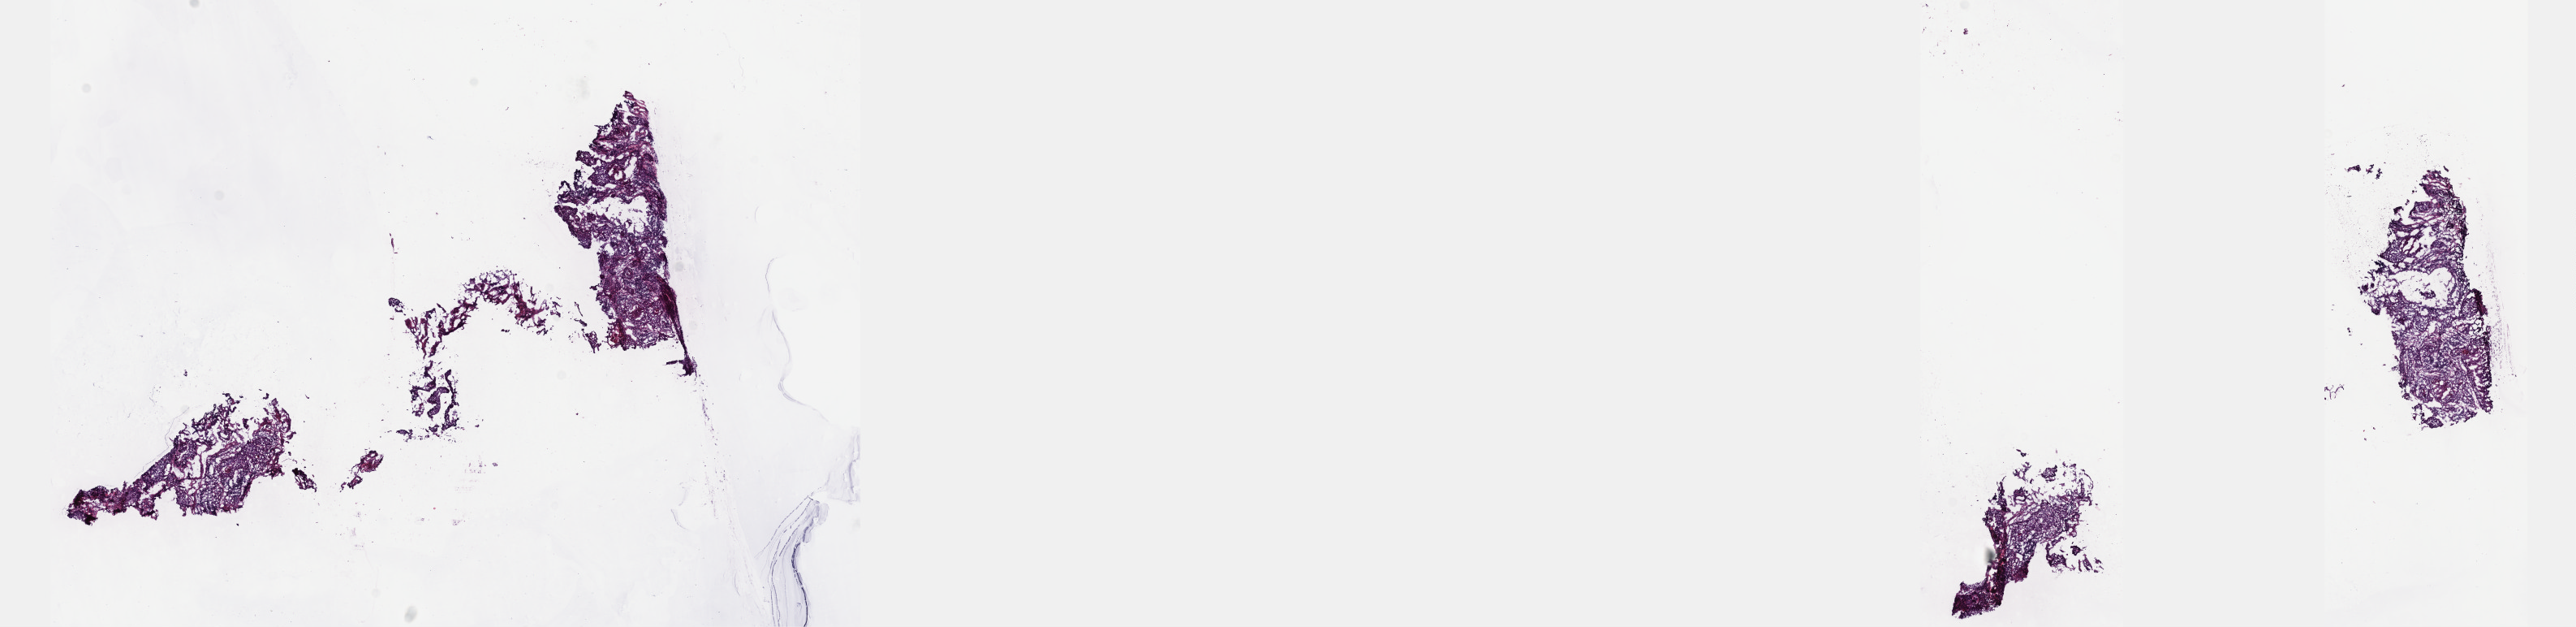
Digitized H&E tissue section (whole slide), low-resolution overview of the scanned area, about 25.7 x 6.2 mm (slide scanned at 40x). Frozen section. Sample: primary tumour, cervix. Female, age 62 years at initial diagnosis. Histologic grade: G3 (poorly differentiated). Slide review estimates, as recorded: tumour cells 80%, tumour nuclei 80%, normal cells 0%, stromal cells 15%, necrosis 5%. Inflammatory infiltration, as recorded: lymphocyte infiltration 40%, monocyte infiltration 20%, neutrophil infiltration 20%.
FIGO stage: IIB. Histologic diagnosis: Squamous cell carcinoma, keratinizing, NOS (cervix uteri).